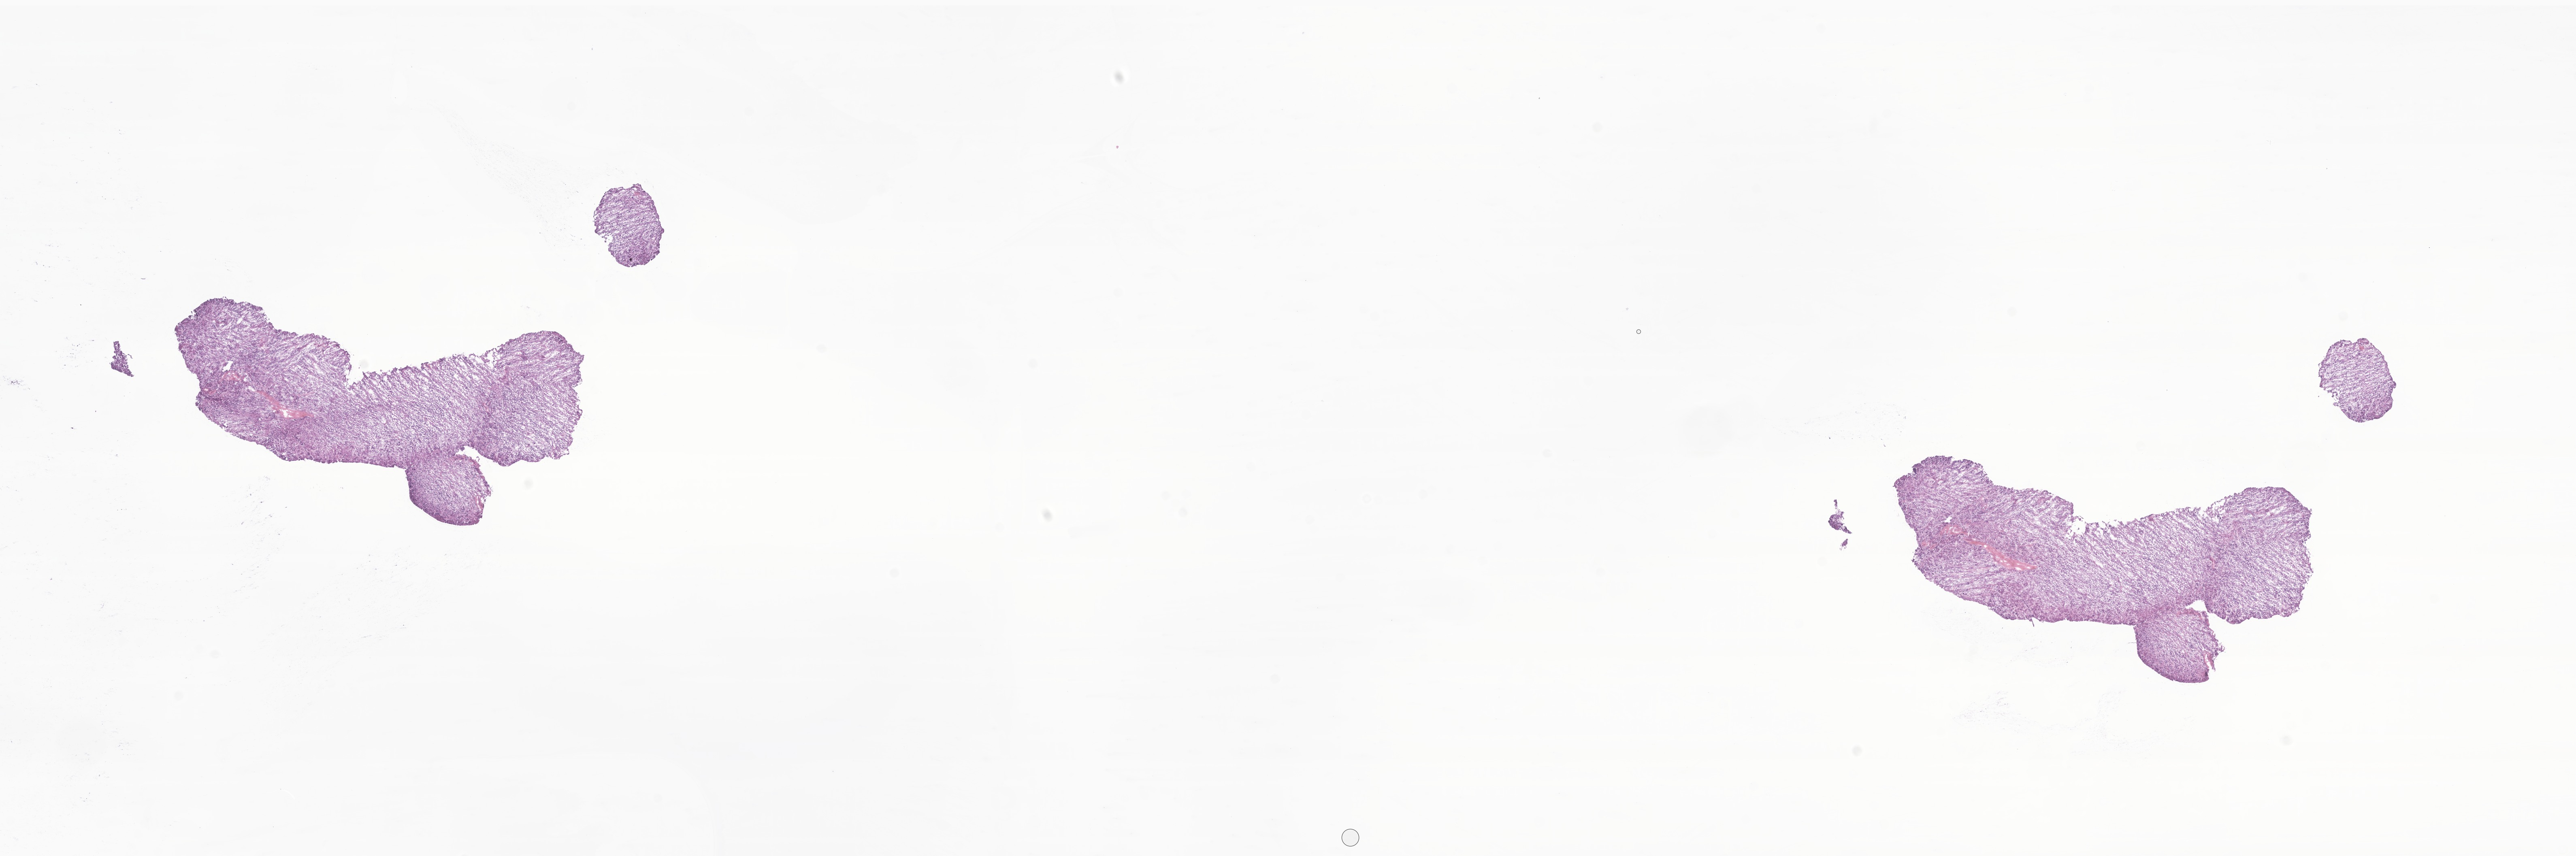
H&E whole-slide image of tumor tissue from the adrenal gland — whole scanned area (about 26.8 x 8.9 mm) shown as a low-resolution overview, frozen section. Patient: female, age 44 months (3 years 8 months).
Diagnosis (ICD-O-3 morphology term): Neuroblastoma, NOS.